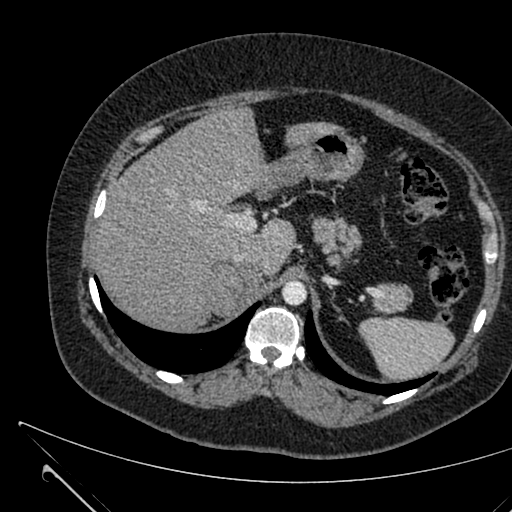
Contrast-enhanced abdominal CT, one axial slice. Slice 478 of 731 in the series (ordered by position). Intravenous contrast given. Soft-tissue window (W 400 / L 40 HU). 1 mm slice thickness. 512 × 512 image matrix, field of view 376 × 376 mm. Female patient, age 36 years. Case-level facts recorded for this patient, not image findings: diagnosis: adrenocortical carcinoma; tumour side: right adrenal; tumour size at pathology: 10 cm; Ki-67 index: 20 %; stage (as recorded): 4.
Structures marked on this image (semi-automatically segmented with operator editing):
- mass: box from (x=217, y=267) to (x=260, y=314) px